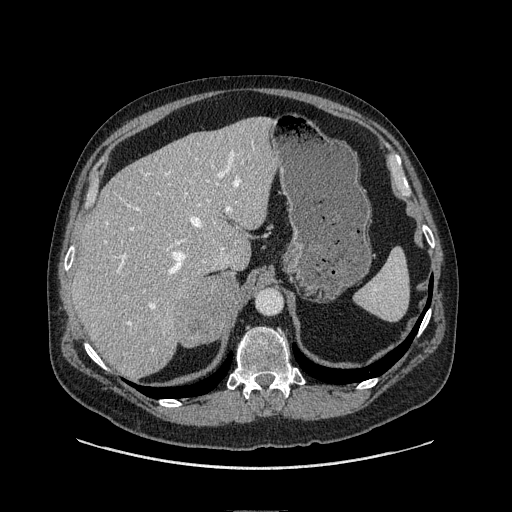
Contrast-enhanced abdominal CT, one axial slice; position 76 of 149 along the scan axis; soft-tissue window (W 400 / L 40 HU); 1.25 mm slice thickness; 512 × 512 image matrix, field of view 440 × 440 mm. Male patient. From the clinical record (not read from this slice): diagnosis: adrenocortical carcinoma; tumour side: right adrenal; tumour size at pathology: 7.5 cm; Ki-67 index: 15 %; stage (as recorded): 2.
Annotated regions visible in this slice (semi-automatic segmentation, software-assisted and operator-edited):
- mass: box from (x=178, y=271) to (x=240, y=347) px